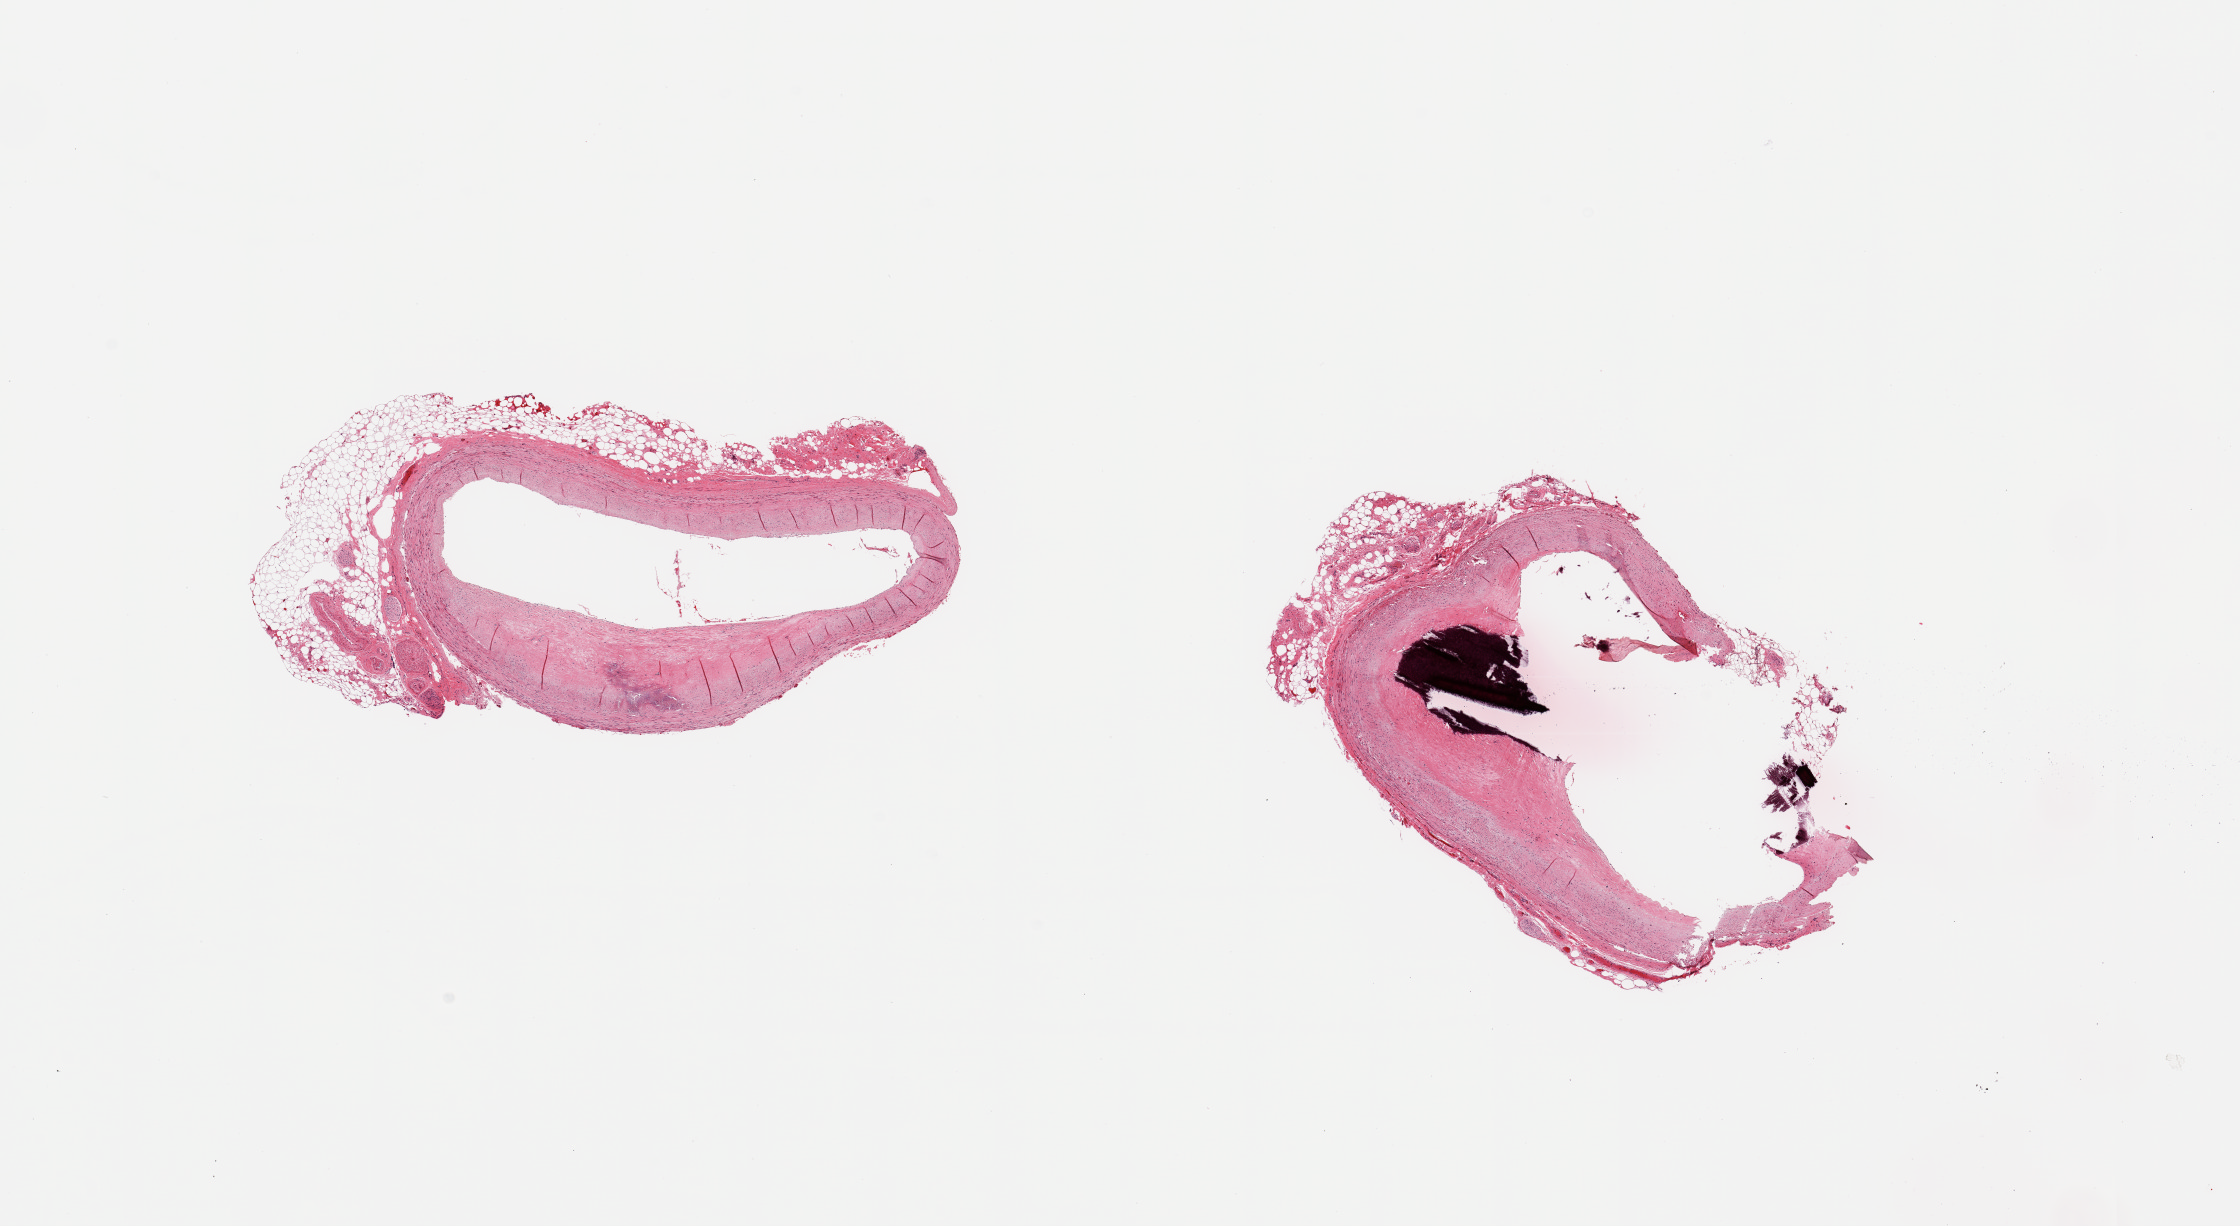
Digitized haematoxylin and eosin-stained section, shown as a low-resolution overview of the whole scanned area (about 17.7 x 9.7 mm, acquisition: 20x scan); PAXgene-fixed paraffin-embedded (PFPE) section; target tissue: coronary artery; tissue donor sample.
Pathologist's review note for this sample: 2 pieces, focally calcified ~40% occlusive atherosis.